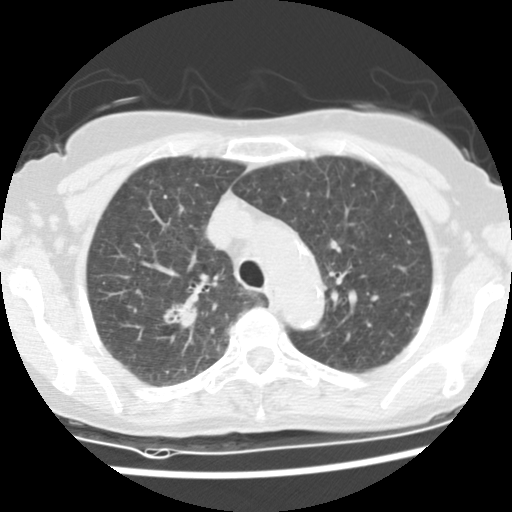
Low-dose screening chest CT, one axial slice; slice 104 of 134 in the series (ordered by position); 120 kVp; lung window (W 1500 / L -600 HU); 2.5 mm slice thickness; 512 × 512 image matrix, field of view 298 × 298 mm.
Annotated regions visible in this slice (expert manual segmentation):
- lesion 1 (tumor, upper lobe of right lung): bounding box [x1, y1, x2, y2] px = [164, 304, 197, 328]